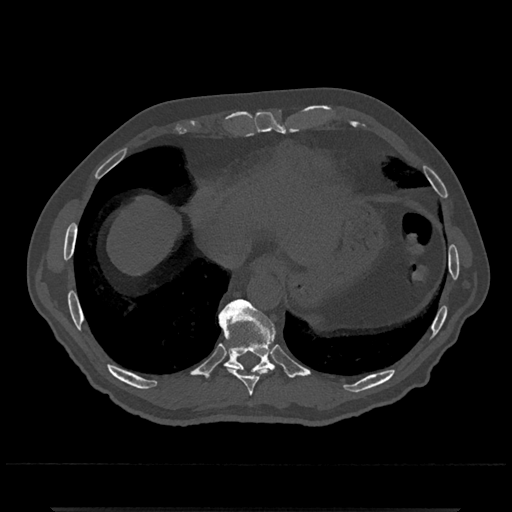
CT including the spine, one axial slice; reconstruction kernel Br40s/3; bone window (W 1800 / L 400 HU); 0.5 mm slice thickness; 512 × 512 image matrix. Patient: male, 67 years. Case-level facts recorded for this patient, not image findings: primary cancer: prostate.
Structures marked on this image (semi-automatically segmented with operator editing):
- T10 vertebra: box from (x=219, y=299) to (x=276, y=373) px
- T9 vertebra: (x=227, y=367)–(x=266, y=396)